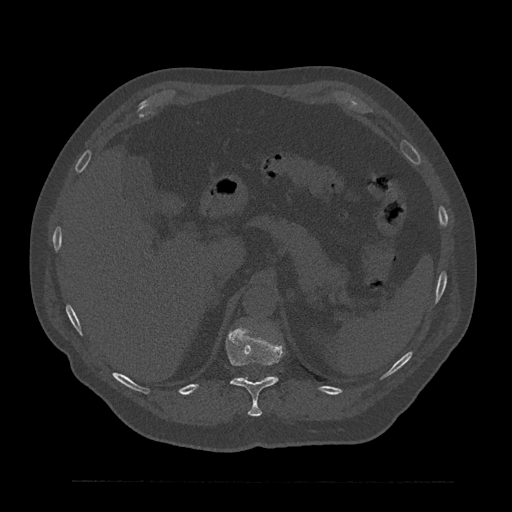
CT including the spine, one axial slice. Position 279 of 797 along the scan axis. Bone window (W 1800 / L 400 HU). 0.5 mm slice thickness. 512 × 512 image matrix. Male patient, age 61 years. Case-level facts recorded for this patient, not image findings: primary cancer: prostate.
Structures marked on this image (semi-automatic segmentation, software-assisted and operator-edited):
- T11 vertebra: bounding box (x1, y1, x2, y2) in pixels: (226, 327, 284, 417)